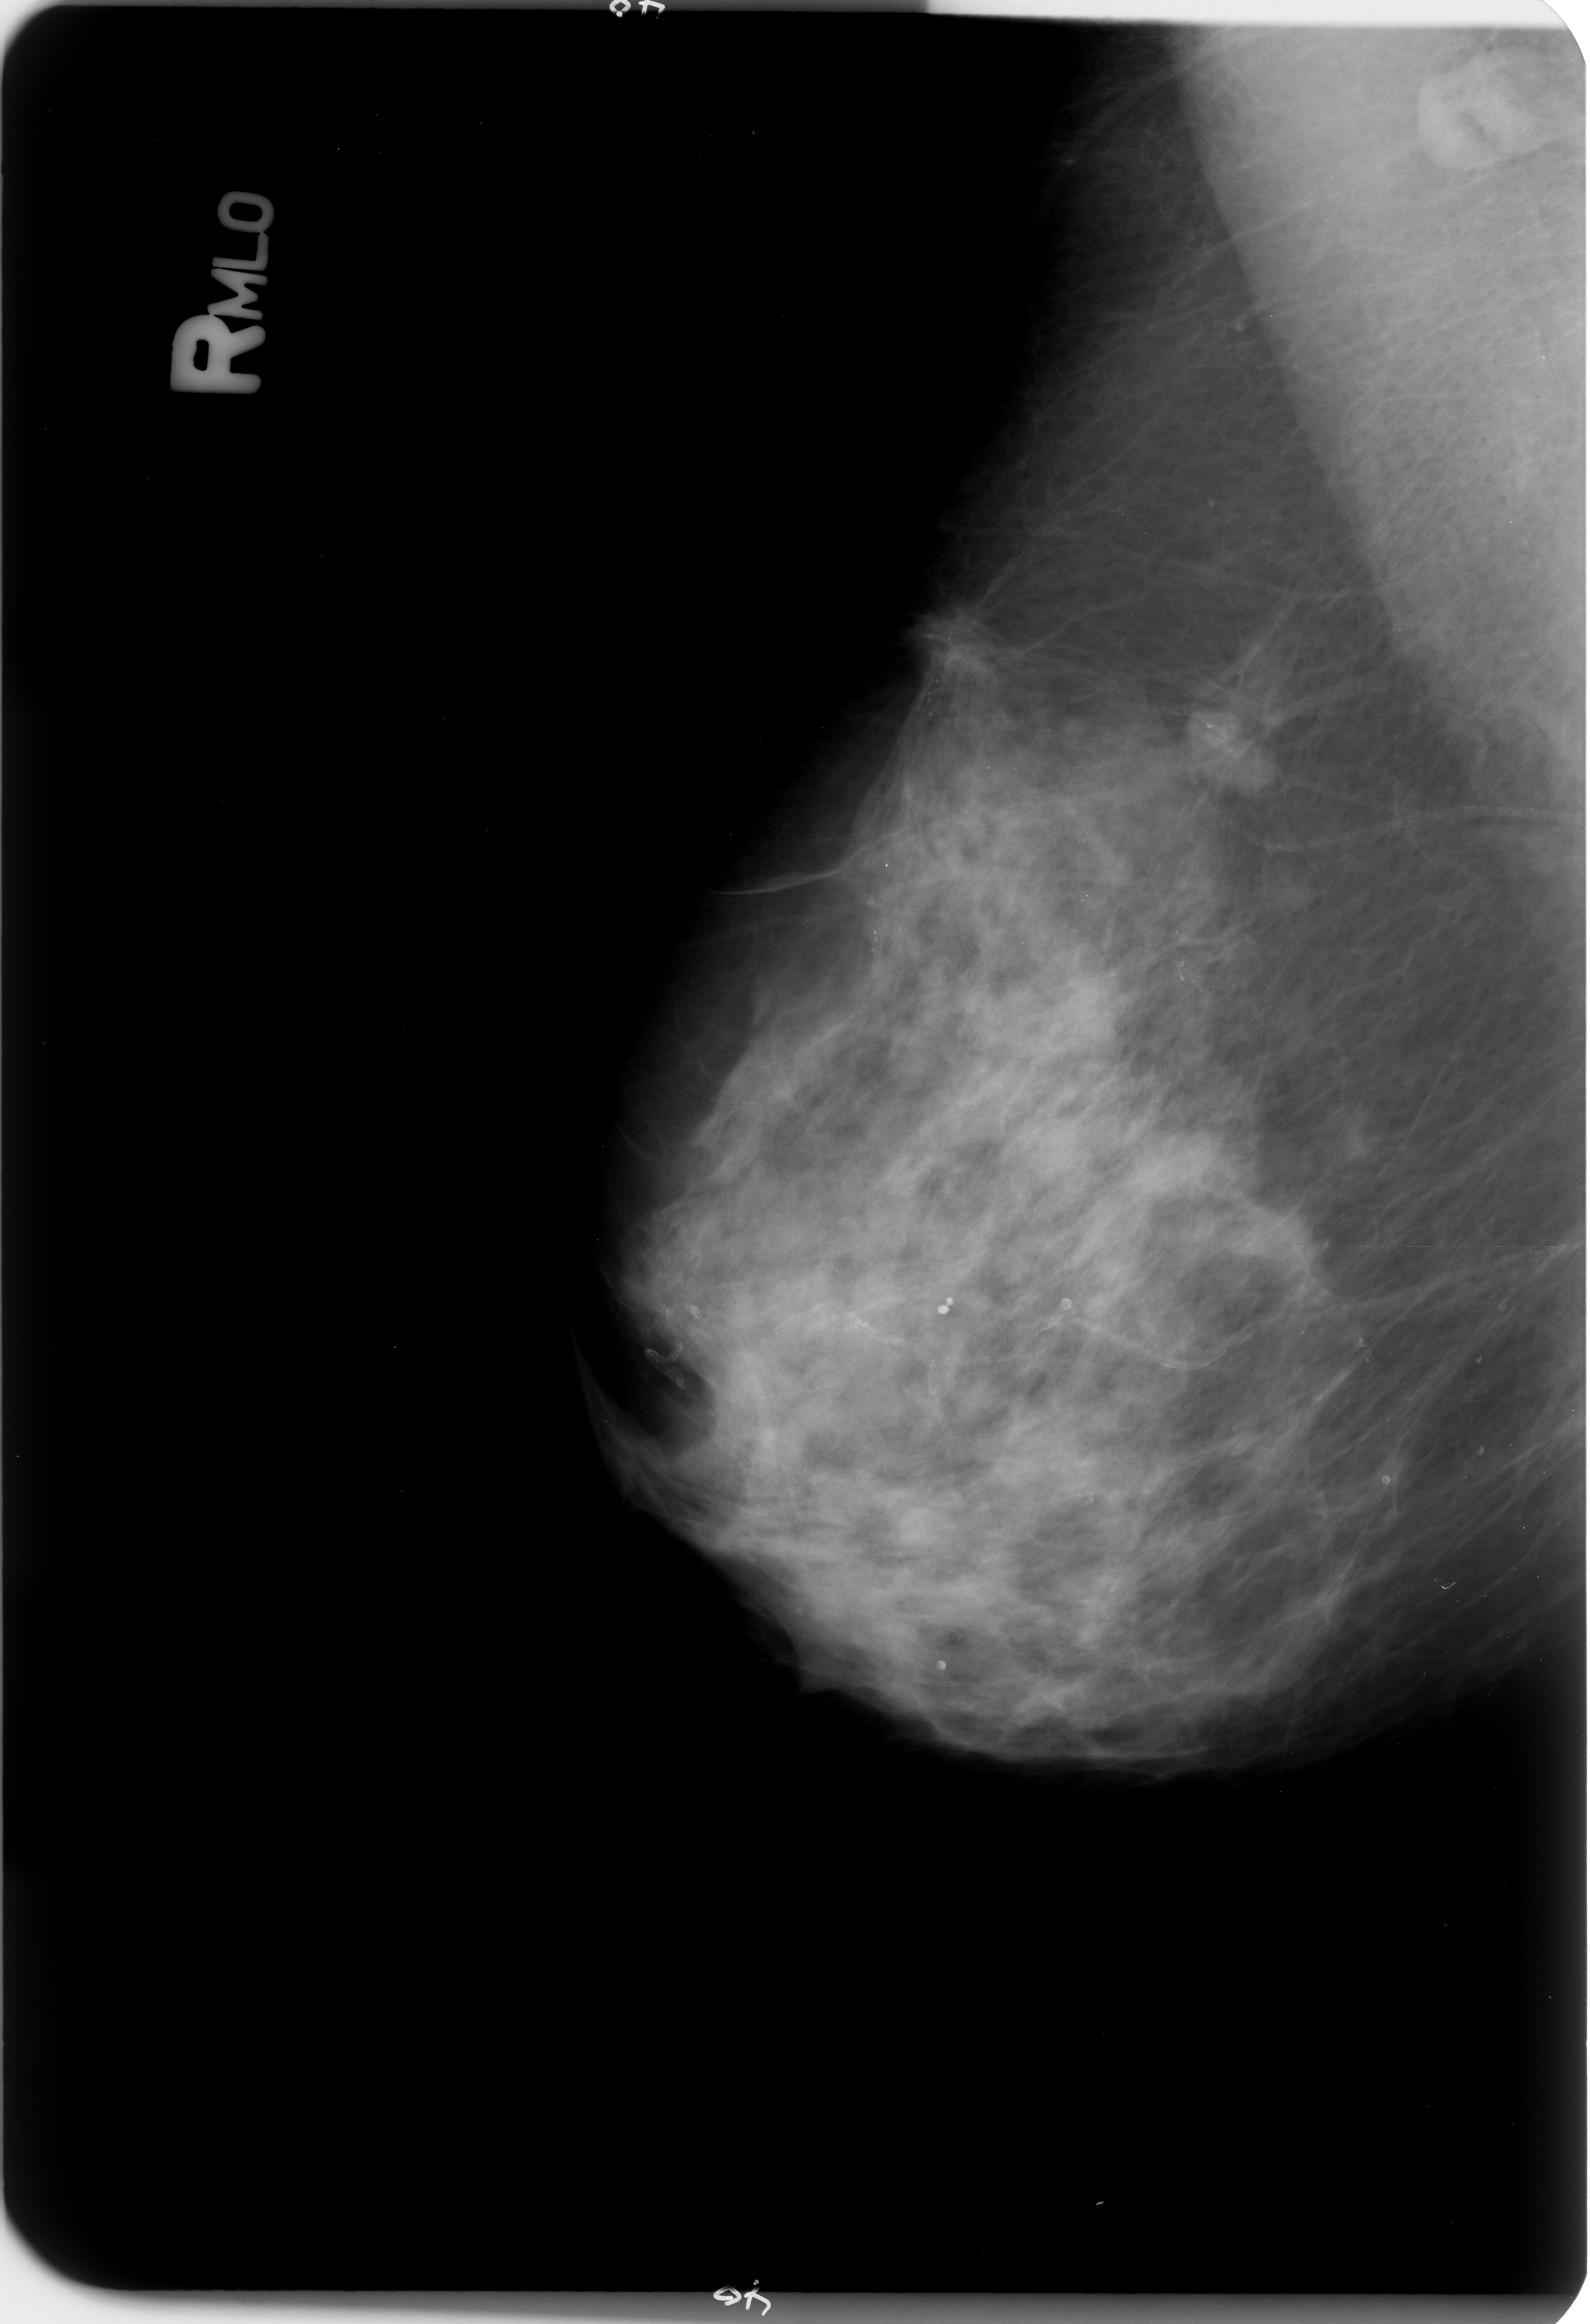
Mammogram (digitized film). Right breast. MLO view. 1590 × 2324 image matrix.
Expert-marked regions of interest on this image (one box per marked abnormality):
- Finding 1 of 2: mass, shape architectural distortion, margins ill defined / spiculated; BI-RADS assessment category 4; pathology result (as recorded, not read from the image): malignant: bounding box (x1, y1, x2, y2) in pixels: (911, 598, 1013, 688)
- Finding 2 of 2: mass, shape architectural distortion, margins ill defined / spiculated; BI-RADS assessment category 4; subtlety rating 4 on a 1 (subtle) to 5 (obvious) scale; pathology result (as recorded, not read from the image): malignant: (1185, 693, 1262, 784)